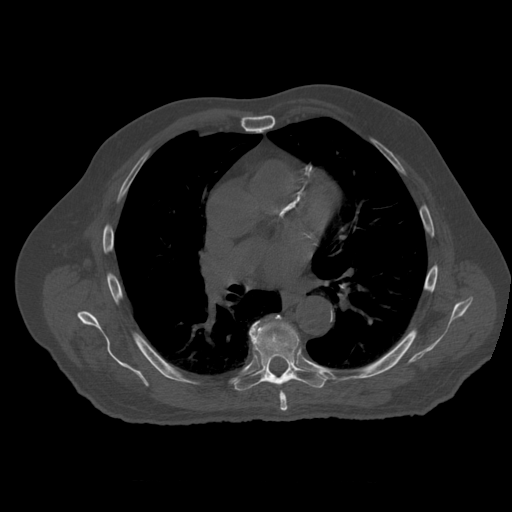
CT including the spine, one axial slice. Slice 368 of 399 in the series (ordered by position). Reconstruction kernel STANDARD. Bone window (W 1800 / L 400 HU). 1.25 mm slice thickness. 512 × 512 image matrix, field of view 407 × 407 mm. Patient age 73 years. Case-level facts recorded for this patient, not image findings: primary cancer: prostate; vertebrae with lytic lesions (as recorded): L2.
Structures marked on this image (semi-automatic segmentation, software-assisted and operator-edited):
- T6 vertebra: bounding box <280,392,288,413> (left, top, right, bottom; pixels)
- T7 vertebra: <235,315,329,391>